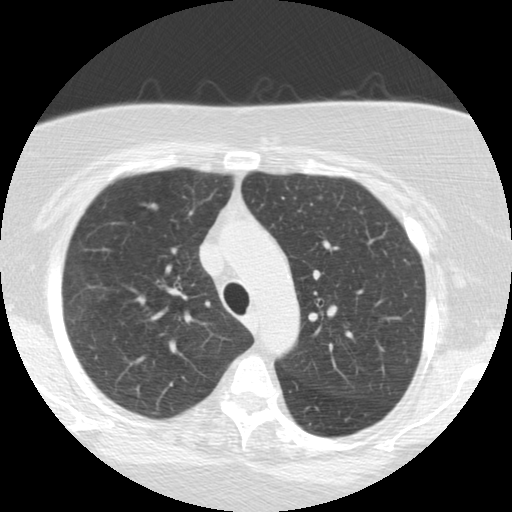
Chest CT (low-dose screening protocol), one axial image. Second screening round (one year after baseline). Lung window (W 1500 / L -600 HU). Female, age 64 years at enrolment. Current smoker at enrolment.
Lesion marked by an expert reader, bounding box (x1, y1, x2, y2) in pixels: (125, 191, 171, 230). The exam's reader record, not a measurement of the box and not confirmed to be the same lesion: non-calcified nodule or mass ≥4 mm, right upper lobe, 8 × 7 mm, smooth margins, soft tissue attenuation, pre-existing on the prior screen: no. Participant outcome: lung cancer diagnosed 85 days after this screen — large cell neuroendocrine carcinoma, right upper lobe, stage IA (AJCC 6th edition), 12 mm at pathology.